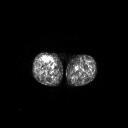
FDG PET of an extremity soft-tissue mass (from a PET/CT study), one axial slice; position 258 of 311 along the scan axis; 3.27 mm slice thickness; 128 × 128 image matrix, field of view 700 × 700 mm. Male patient, age 56 years. Case-level facts recorded for this patient, not image findings: histological type: pleiomorphic leiomyosarcoma; grade: intermediate; site of the primary tumour: right thigh.
Structures marked on this image (expert contour drawn on MRI and transferred to this co-registered scan by the dataset authors):
- gross tumour volume including surrounding oedema: bounding box <42,56,51,62> (left, top, right, bottom; pixels)